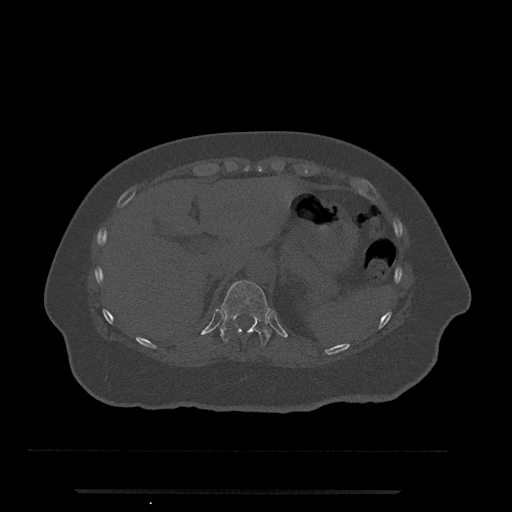
CT including the spine, one axial slice; slice 241 of 797 in the series (ordered by position); 120 kVp; bone window (W 1800 / L 400 HU); 0.5 mm slice thickness; 512 × 512 image matrix, field of view 440 × 440 mm. Patient: female, 51 years. From the clinical record (not read from this slice): primary cancer: neuro; vertebrae with lytic lesions (as recorded): T8.
Structures marked on this image (semi-automatically segmented with operator editing):
- T11 vertebra: bounding box [x1, y1, x2, y2] px = [220, 280, 272, 346]